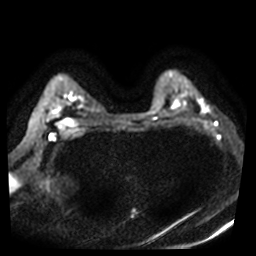
Breast MRI, one axial slice. Slice 31 of 40 in the series (ordered by position). Diffusion-weighted series; image 2 of 4 stored at this slice position (different b-values; order by instance number). 3 T. 256 × 256 image matrix, field of view 360 × 360 mm. Female patient.
Outlined on this slice (manually delineated by an expert):
- tumour on diffusion-weighted imaging: bounding box [x1, y1, x2, y2] px = [202, 105, 208, 111]